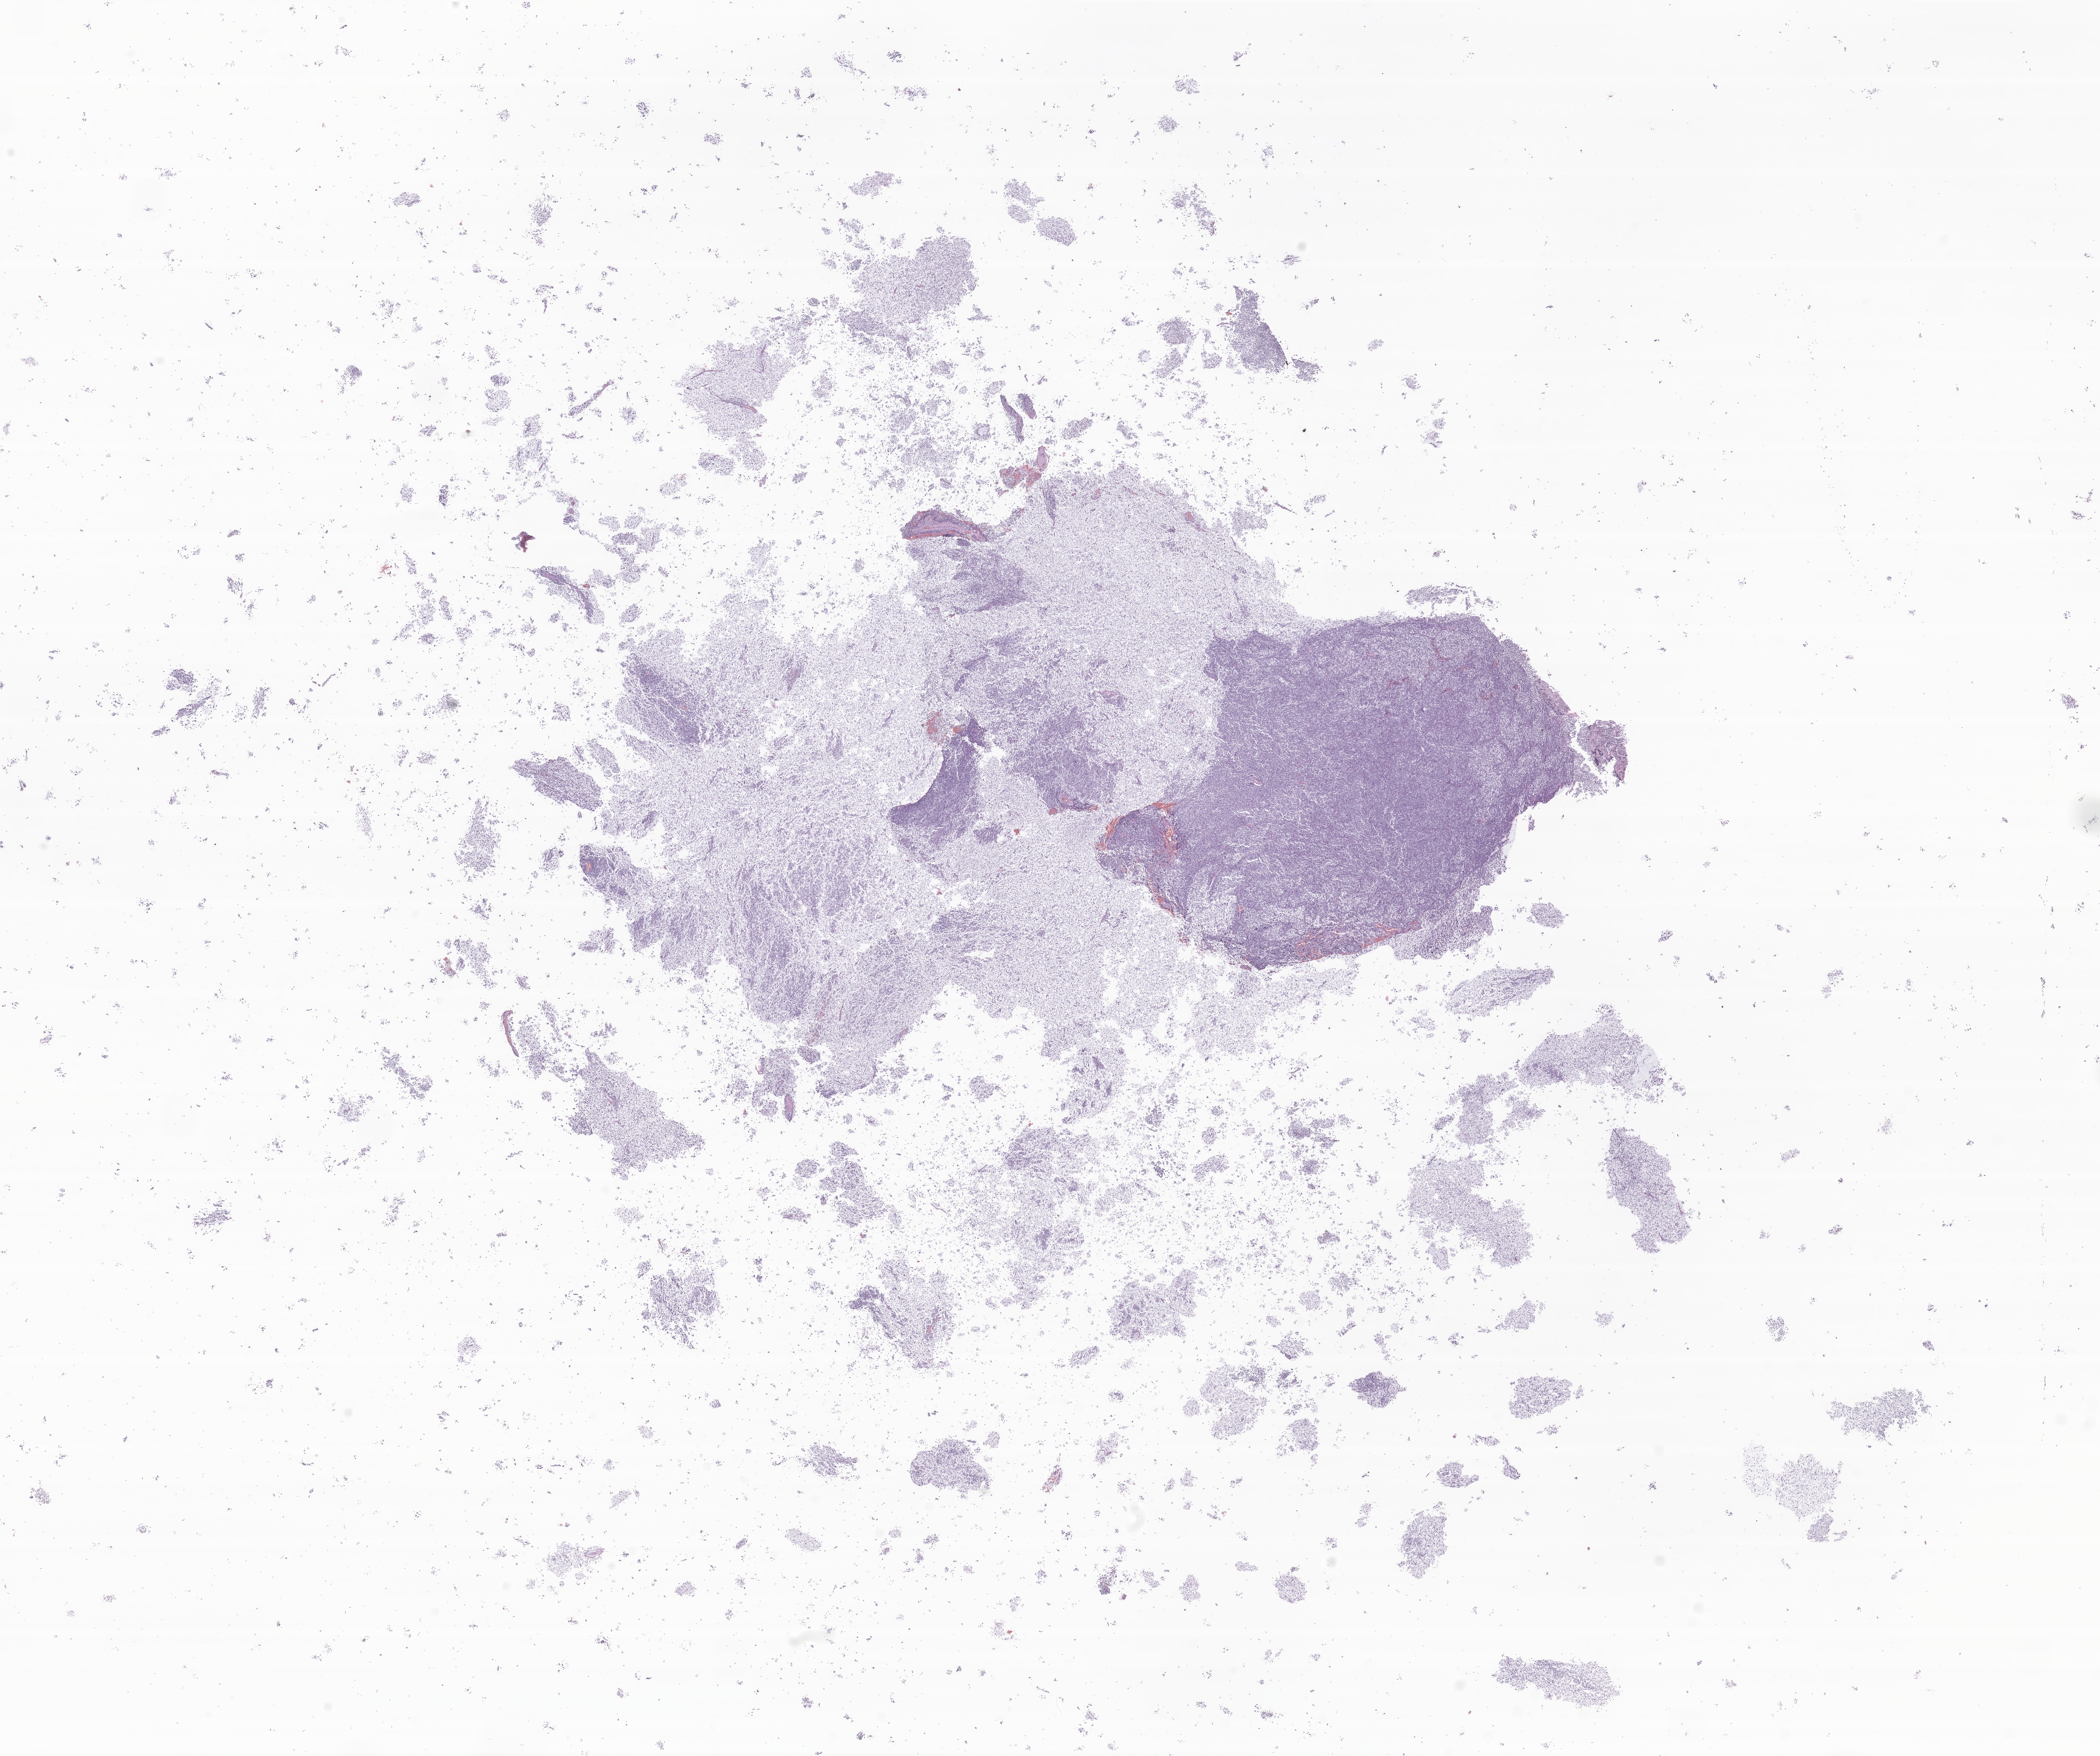
Haematoxylin and eosin whole-slide image of tumor tissue from the cerebellum, whole scanned area (about 24.6 x 20.5 mm) shown as a low-resolution overview. Formalin-fixed paraffin-embedded section. Patient male; age 87 months.
Diagnosis (ICD-O-3 morphology term): Medulloblastoma, NOS.